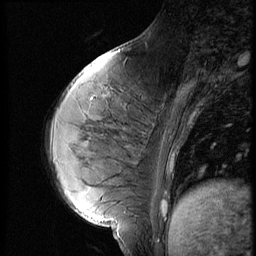
Breast MRI (dynamic contrast-enhanced), one sagittal slice. Position 19 of 56 along the scan axis. 3 images stored at this slice position (order not interpretable as contrast timing). 1.5 T. TE 4.2 ms, TR 9 ms. 2.5 mm slice thickness. 256 × 256 image matrix. Patient: female, 35 years. Case-level facts recorded for this patient, not image findings: setting: breast cancer imaged before/during neoadjuvant chemotherapy; receptor status: HR-positive, HER2-negative.
Annotated regions visible in this slice (semi-automatically segmented with operator editing):
- analysis volume of interest (the breast-tissue region the enhancement analysis was run in; not a lesion): bounding box (x1, y1, x2, y2) in pixels: (58, 70, 171, 208)
- tumour enhancement mask (voxels above the 140 % enhancement threshold inside the analysis volume of interest): (162, 201, 167, 208)